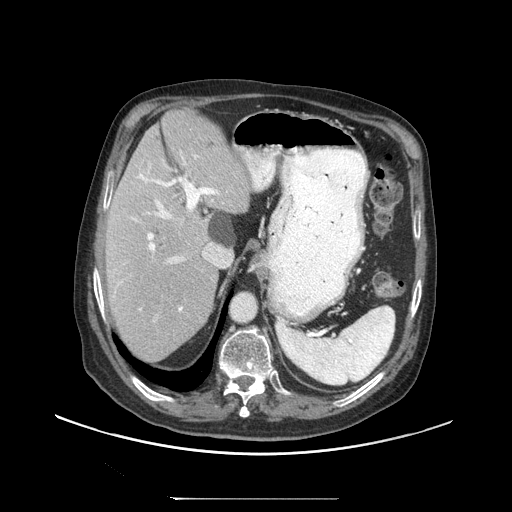
Contrast-enhanced abdominal CT (liver protocol), one axial slice; position 70 of 97 along the scan axis; reconstruction kernel STANDARD; 140 kVp; soft-tissue window (W 400 / L 40 HU); 512 × 512 image matrix. Case-level facts recorded for this patient, not image findings: diagnosis: hepatocellular carcinoma (patient treated with transarterial chemoembolisation; whether this scan precedes or follows treatment is not stated here); TNM stage (as recorded): Stage-IIIC; Child-Pugh class: A.
Outlined on this slice (semi-automatic segmentation, software-assisted and operator-edited):
- abdominal aorta: box from (x=231, y=293) to (x=256, y=321) px
- liver parenchyma outside the tumour (the mass and vessels are separate outlines, so this box may not span the whole liver): (x=106, y=109)–(x=250, y=360)
- liver vessels: (x=132, y=155)–(x=218, y=311)